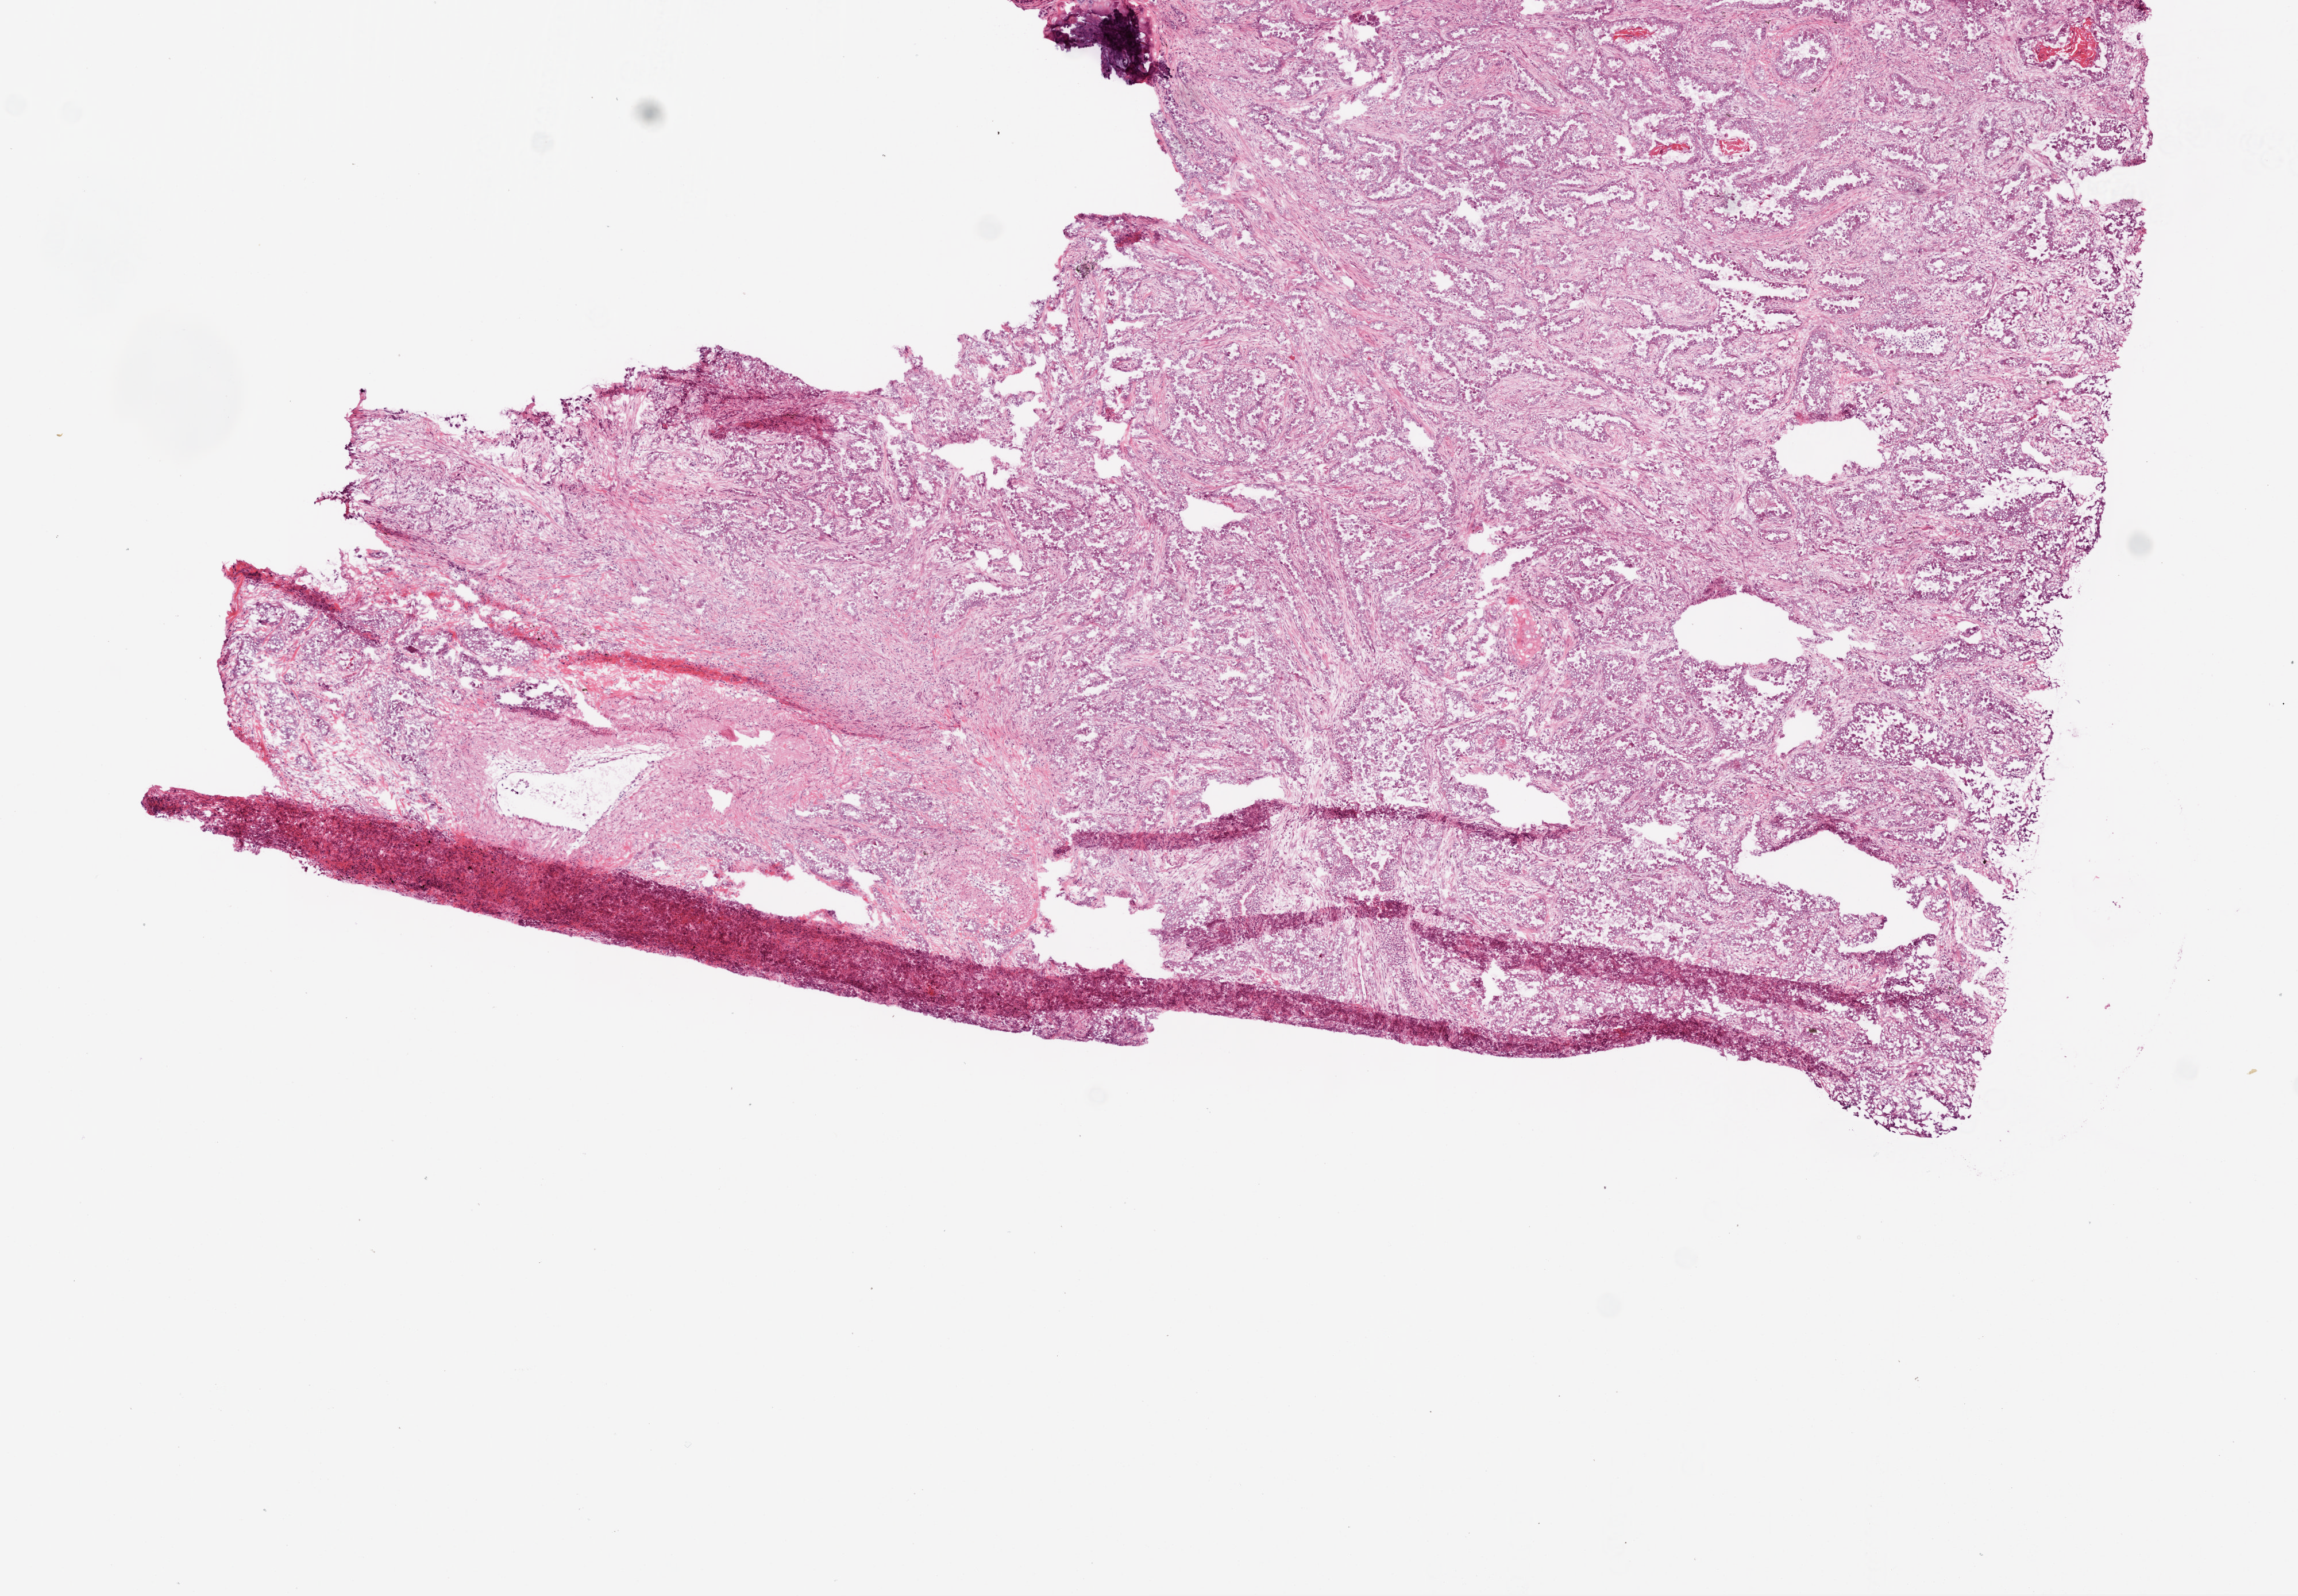
H&E-stained whole-slide image — shown as a low-resolution overview of the whole scanned area (about 8.0 x 5.6 mm, acquisition: 20x scan). Frozen section from the top of the tissue portion. Primary tumour sample from the lung. Female patient; age at initial diagnosis 65 years. Pathologist review of this section (percent, as recorded): tumour cells 80%, tumour nuclei 75%, normal cells 0%, stromal cells 20%, necrosis 0%.
• histologic diagnosis: Adenocarcinoma, NOS
• AJCC pathologic stage: IIB